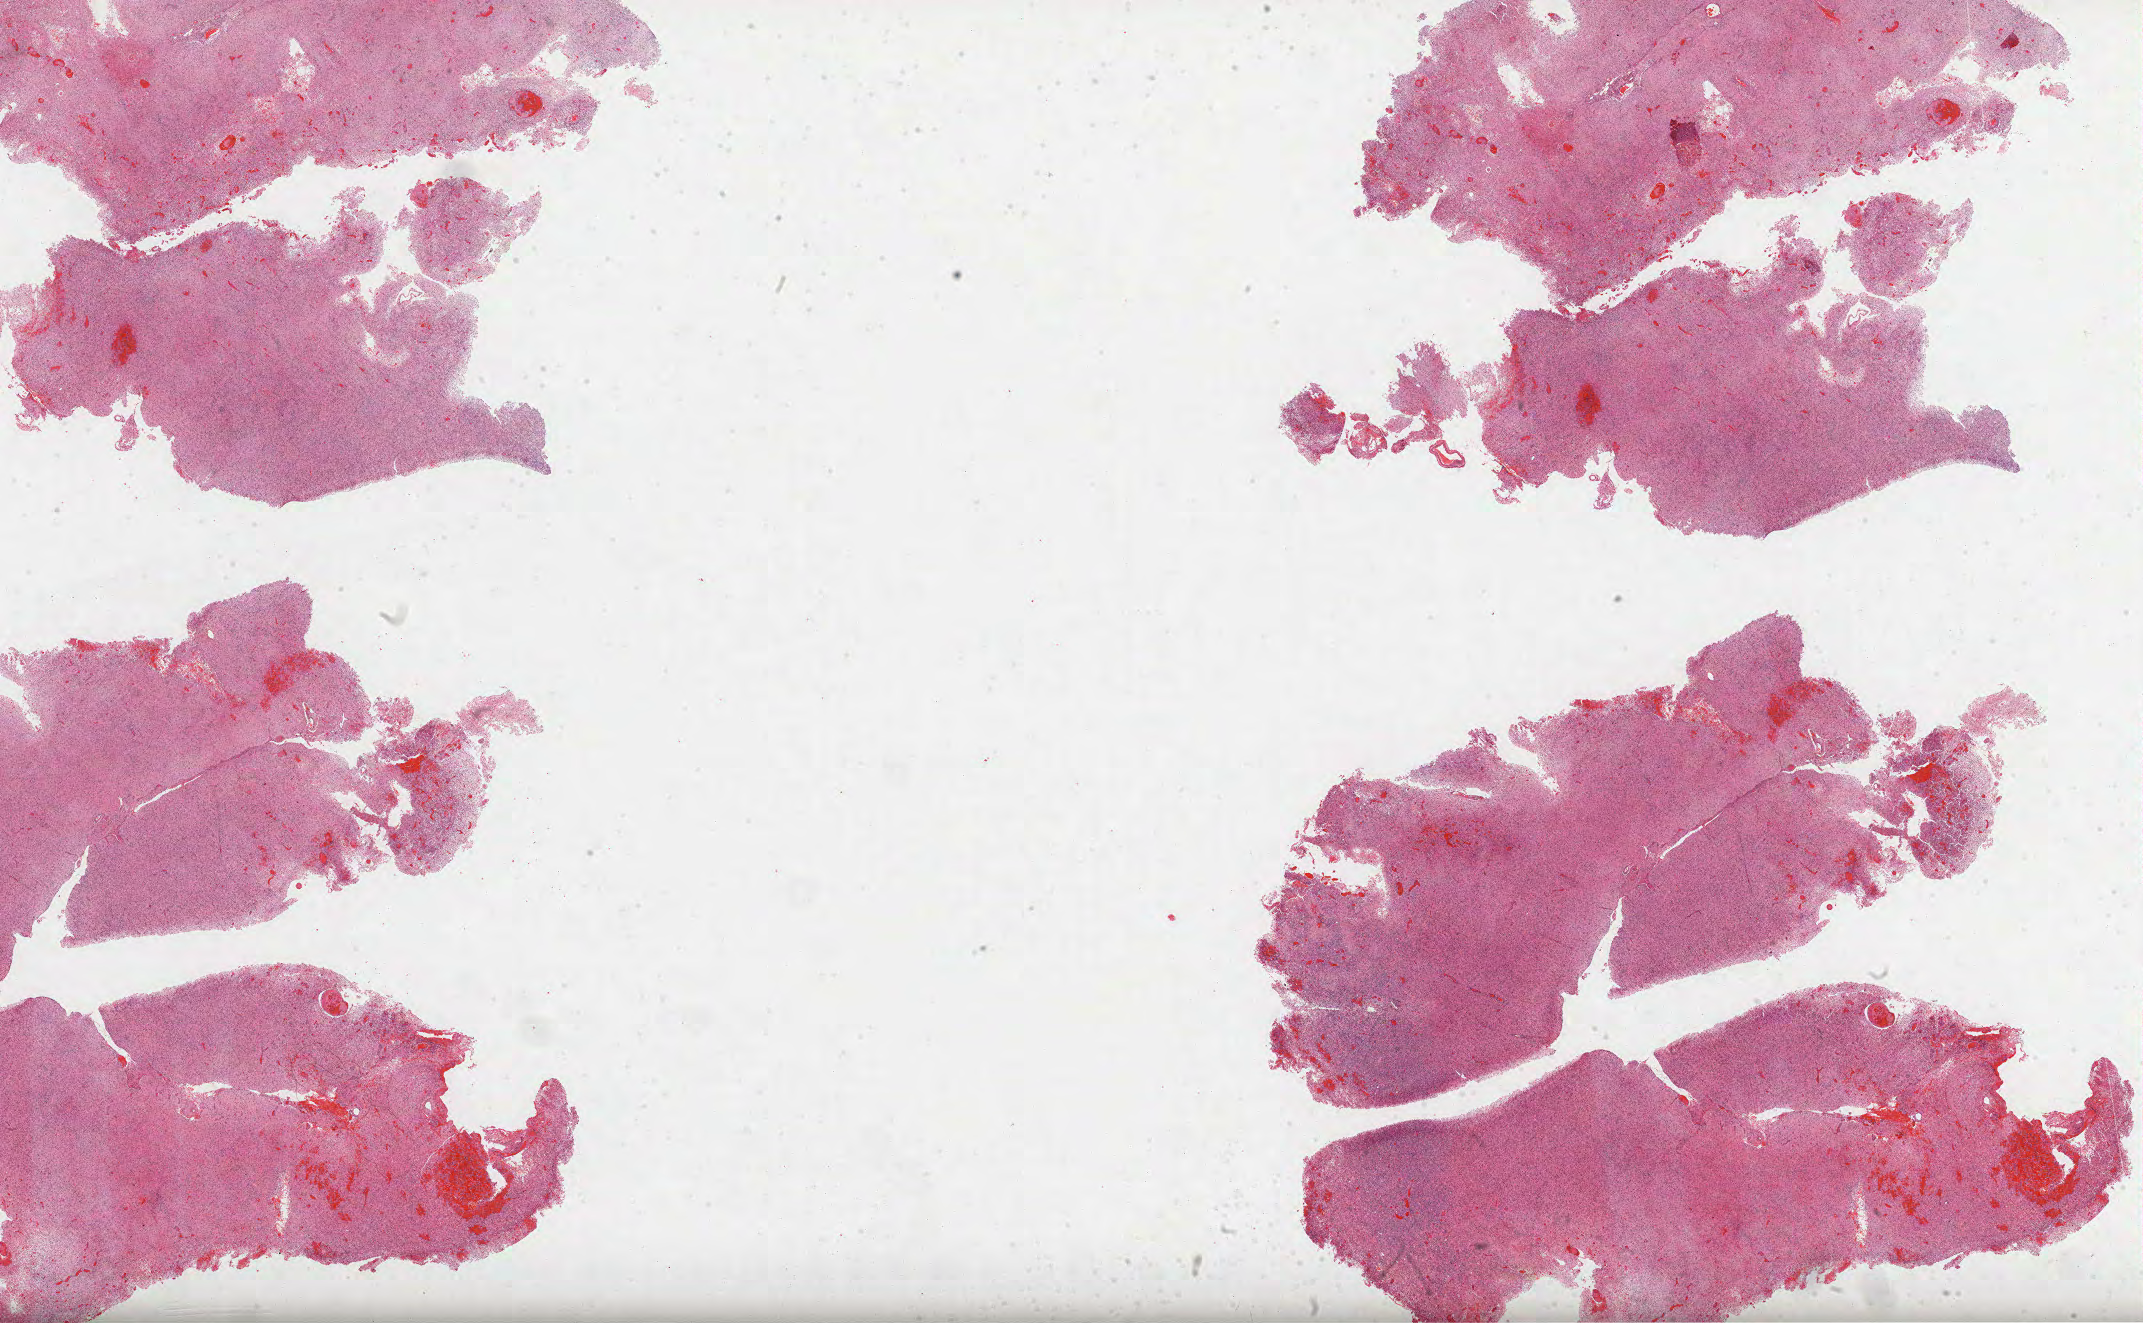
Digitized Hematoxylin and eosin (H&E) stained tissue section (whole slide) — whole scanned area (about 34.6 x 21.3 mm) shown as a low-resolution overview. Formalin-fixed paraffin-embedded (FFPE) diagnostic section. Sample: primary tumour, brain. Male, age 62 years at initial diagnosis.
Pathologic diagnosis: Glioblastoma.